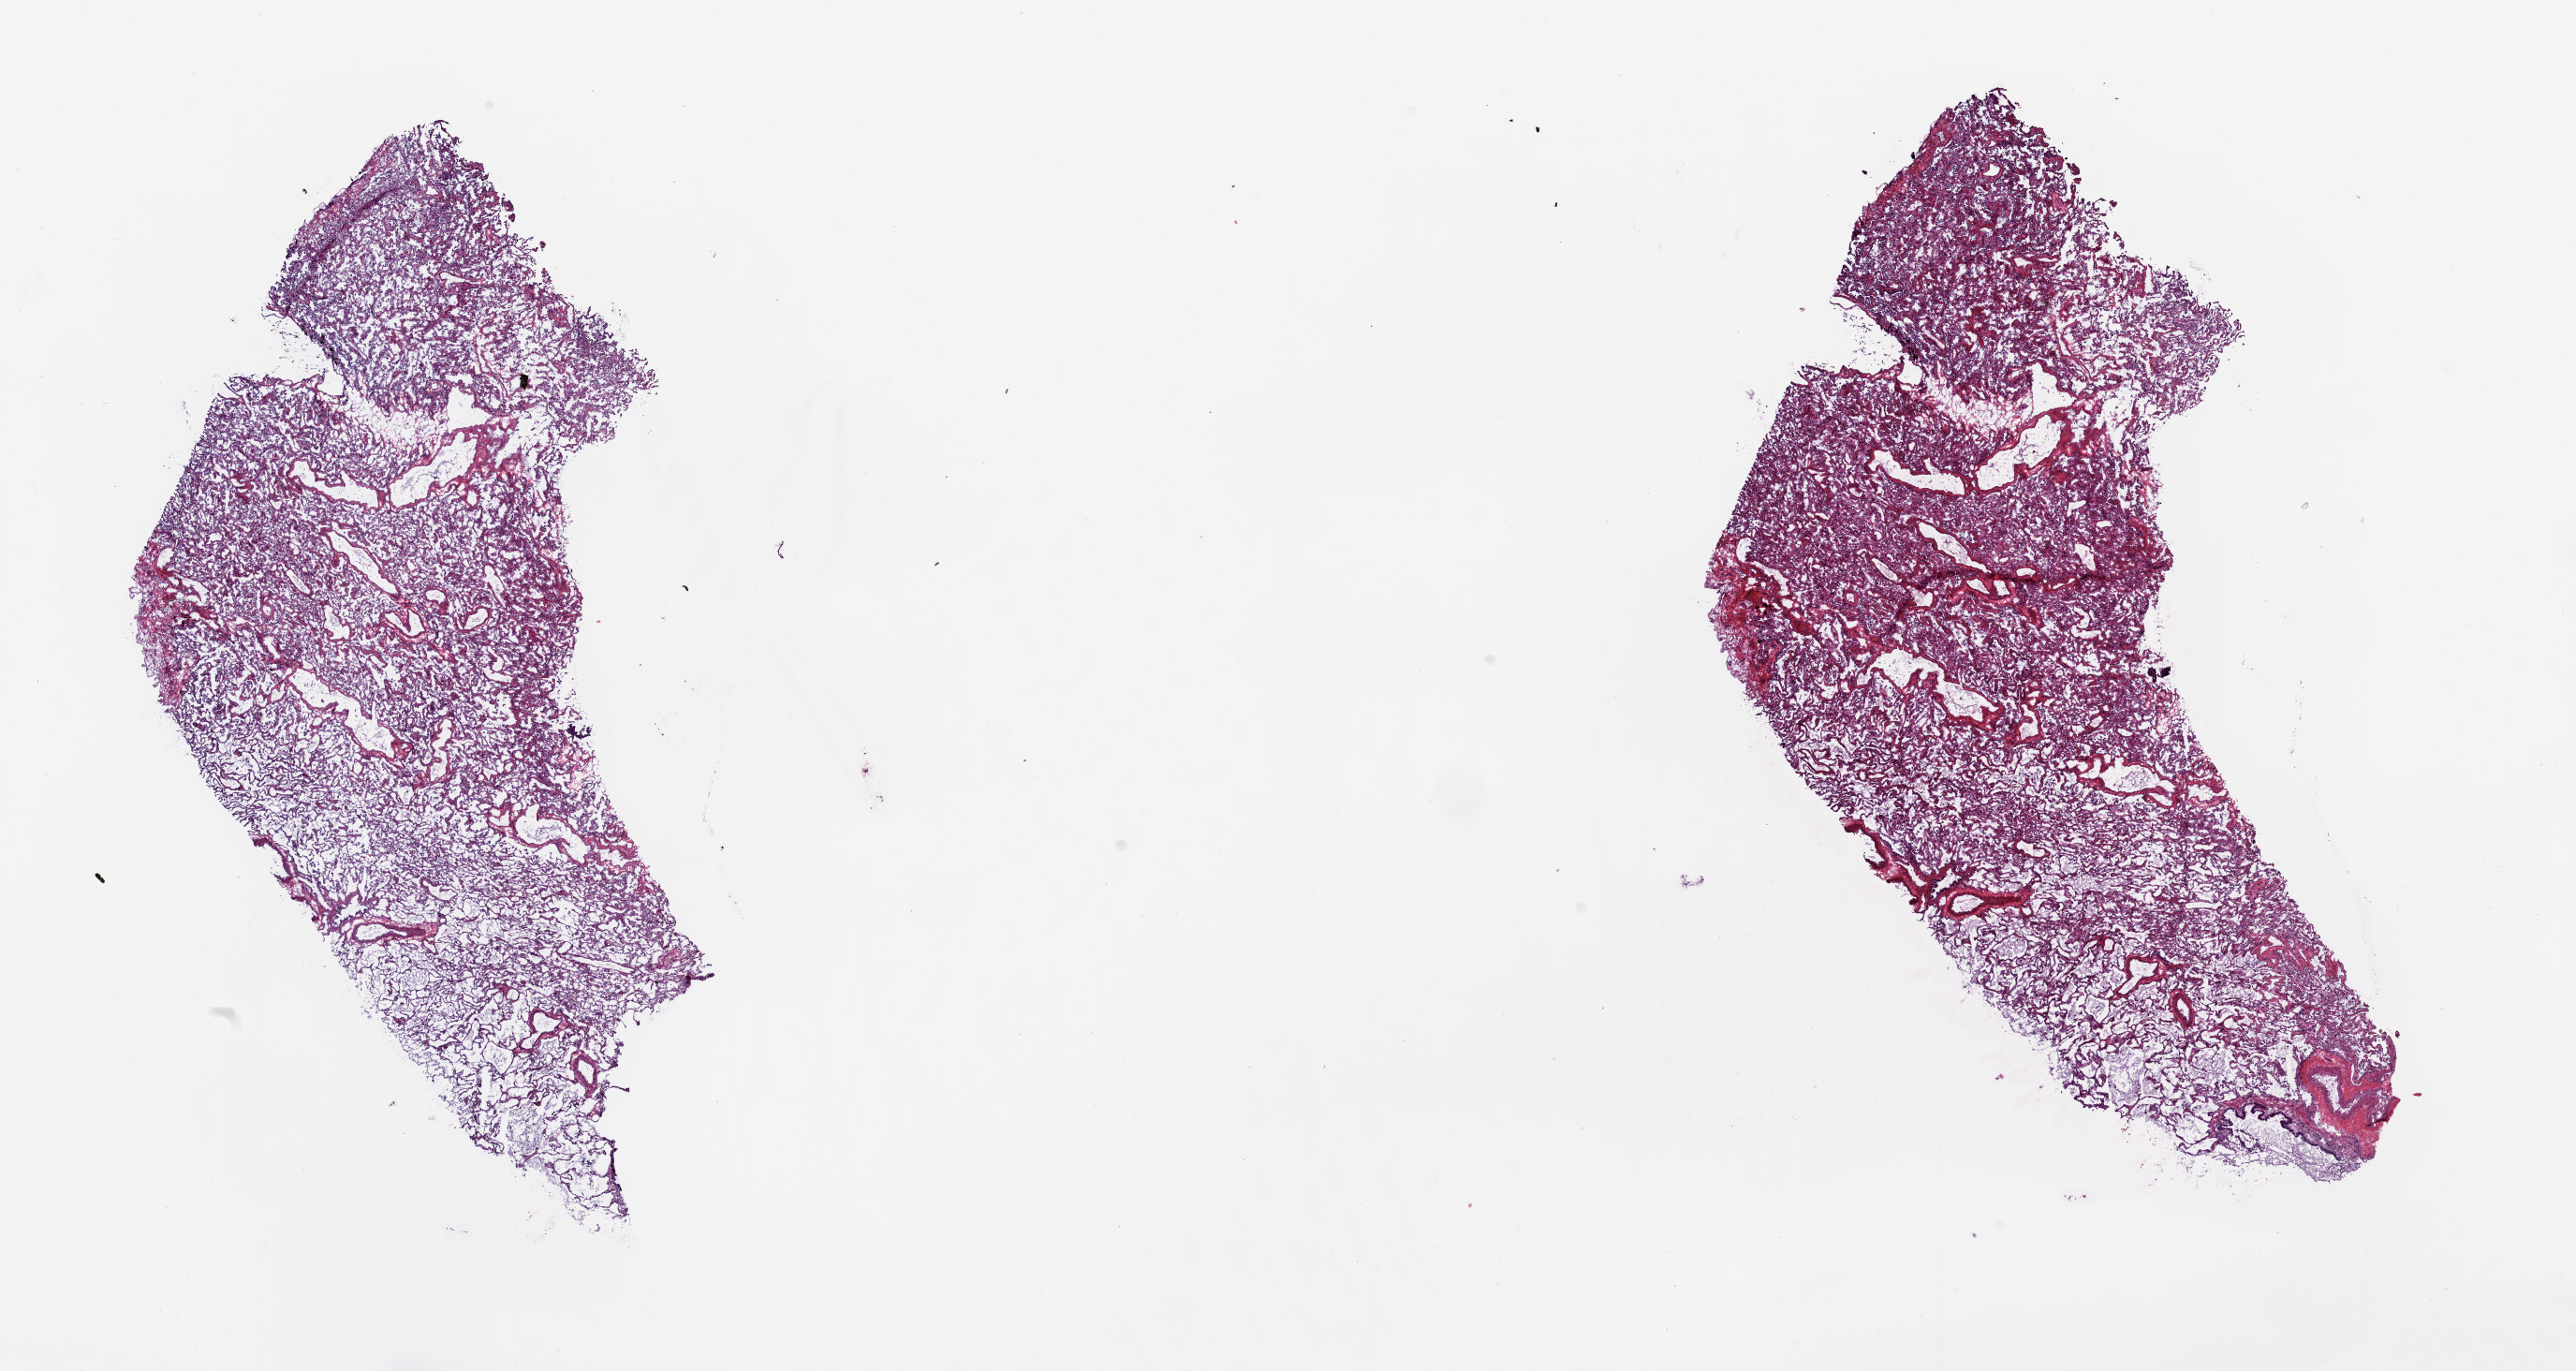
Digitized H&E-stained tissue section (whole slide) — whole scanned area (about 21.8 x 11.6 mm, from a 20x scan) shown as a low-resolution overview; frozen section; lung, solid tissue normal (non-tumour tissue) sample. Patient: male, age at initial diagnosis 64 years. Pathologist review of this section (percent, as recorded): tumour cells 0%, tumour nuclei 0%, normal cells 60%, stromal cells 40%, necrosis 0%. Infiltration values recorded for this section: lymphocyte infiltration 3%, monocyte infiltration 7%, neutrophil infiltration 2%.
This section: solid tissue normal (non-tumour) sample from the same patient. Patient diagnosis: Acinar cell carcinoma (lower lobe, lung).